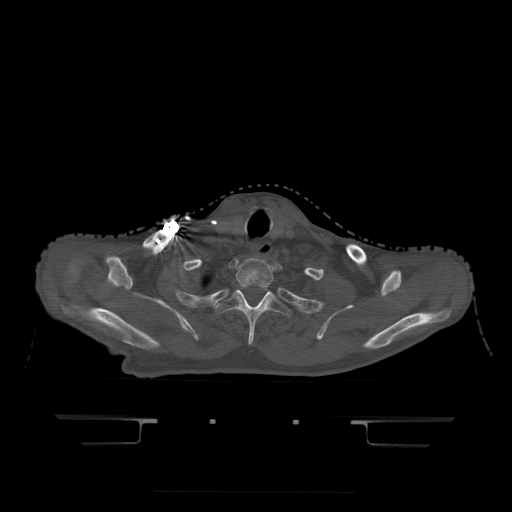
CT including the spine, one axial slice; position 391 of 522 along the scan axis; bone window (W 1800 / L 400 HU); 1.25 mm slice thickness; 512 × 512 image matrix. Patient age 68 years. From the clinical record (not read from this slice): primary cancer: urothelial.
Outlined on this slice (semi-automatically segmented with operator editing):
- T1 vertebra: bounding box [x1, y1, x2, y2] px = [236, 259, 274, 289]
- T2 vertebra: [217, 287, 292, 346]